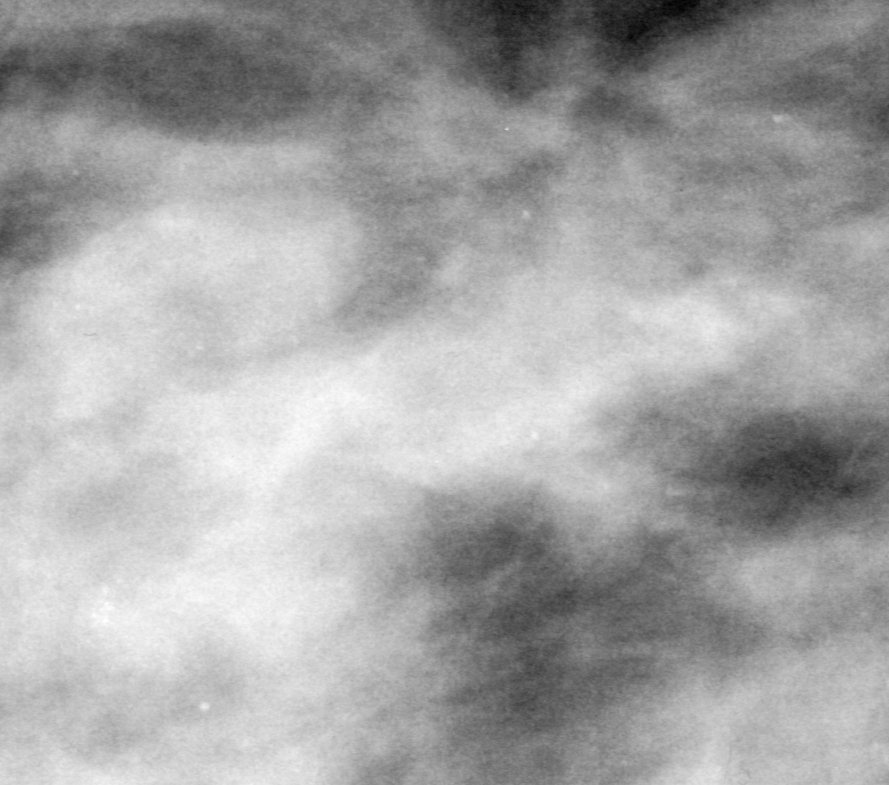
Region of interest cut from a scanned film mammogram (one marked finding); left breast; MLO view; BI-RADS breast density category 4 (scale 1–4).
Marked abnormality: calcifications, morphology pleomorphic, distribution segmental; BI-RADS assessment category 4; pathology result (as recorded, not read from the image): malignant.